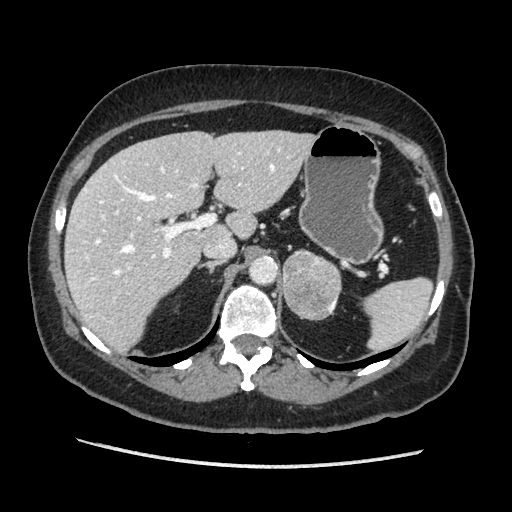
Contrast-enhanced abdominal CT, one axial slice; position 130 of 203 along the scan axis; soft-tissue window (W 400 / L 40 HU); 512 × 512 image matrix, field of view 360 × 360 mm. Female patient. From the clinical record (not read from this slice): diagnosis: adrenocortical carcinoma; tumour side: left adrenal; tumour size at pathology: 6.5 cm; Ki-67 index: 22 %; stage (as recorded): 2.
Annotated regions visible in this slice (semi-automatically segmented with operator editing):
- mass: bounding box <282,250,341,319> (left, top, right, bottom; pixels)